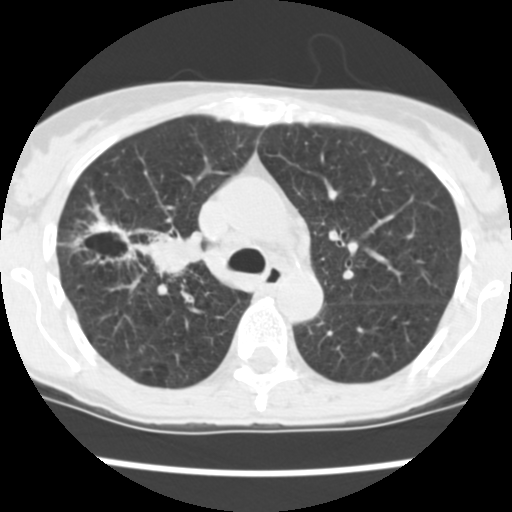
Low-dose screening chest CT, axial slice. Baseline annual screen. Lung window (W 1500 / L -600 HU). 2.5 mm slice thickness. 120 kVp. Slice 167 of 252 in the series. Female participant, aged 60 years at enrolment.
Expert reader's lesion annotation, bounding box (x1, y1, x2, y2) in pixels: (83, 216, 193, 283). The screening reader recorded 3 non-calcified nodules or masses ≥4 mm on this exam (right upper lobe, right upper lobe, right lower lobe); which of them this box marks is not recorded. Participant outcome: lung cancer diagnosed 19 days after this screen — non-small cell carcinoma, right upper lobe, stage IV (AJCC 6th edition), 26 mm at pathology.